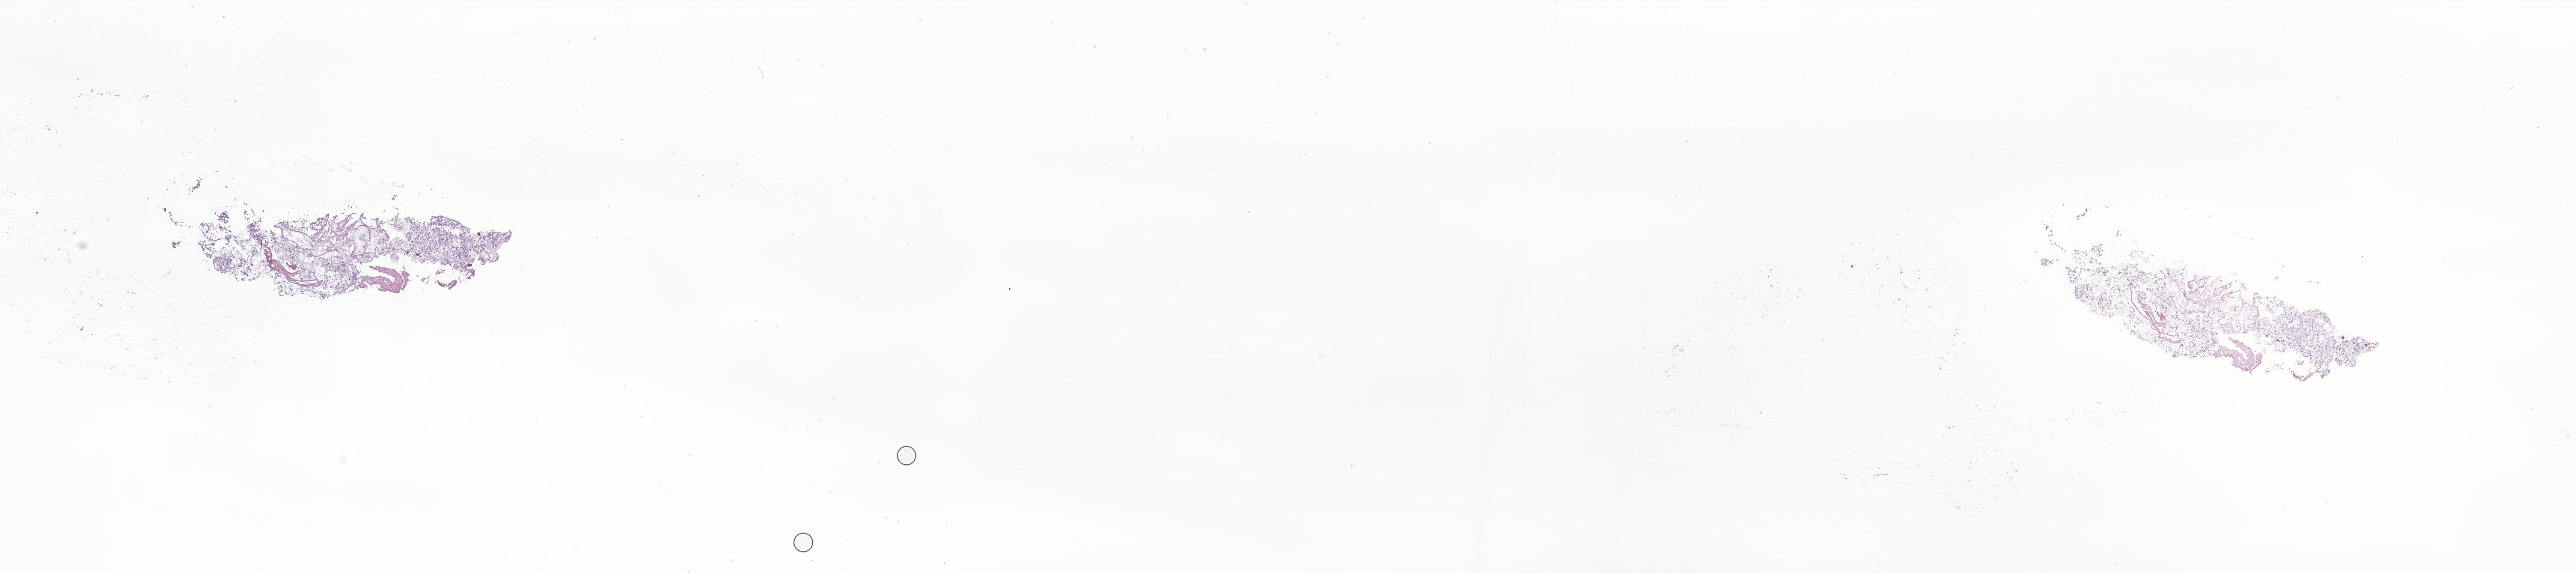
H&E whole-slide image of tumor tissue from the brain, a low-resolution overview of the entire scanned area, about 25.4 x 5.6 mm. Frozen section (OCT-embedded). Patient male; age 178 months (14 years 10 months).
Recorded diagnosis: Neoplasm, malignant.